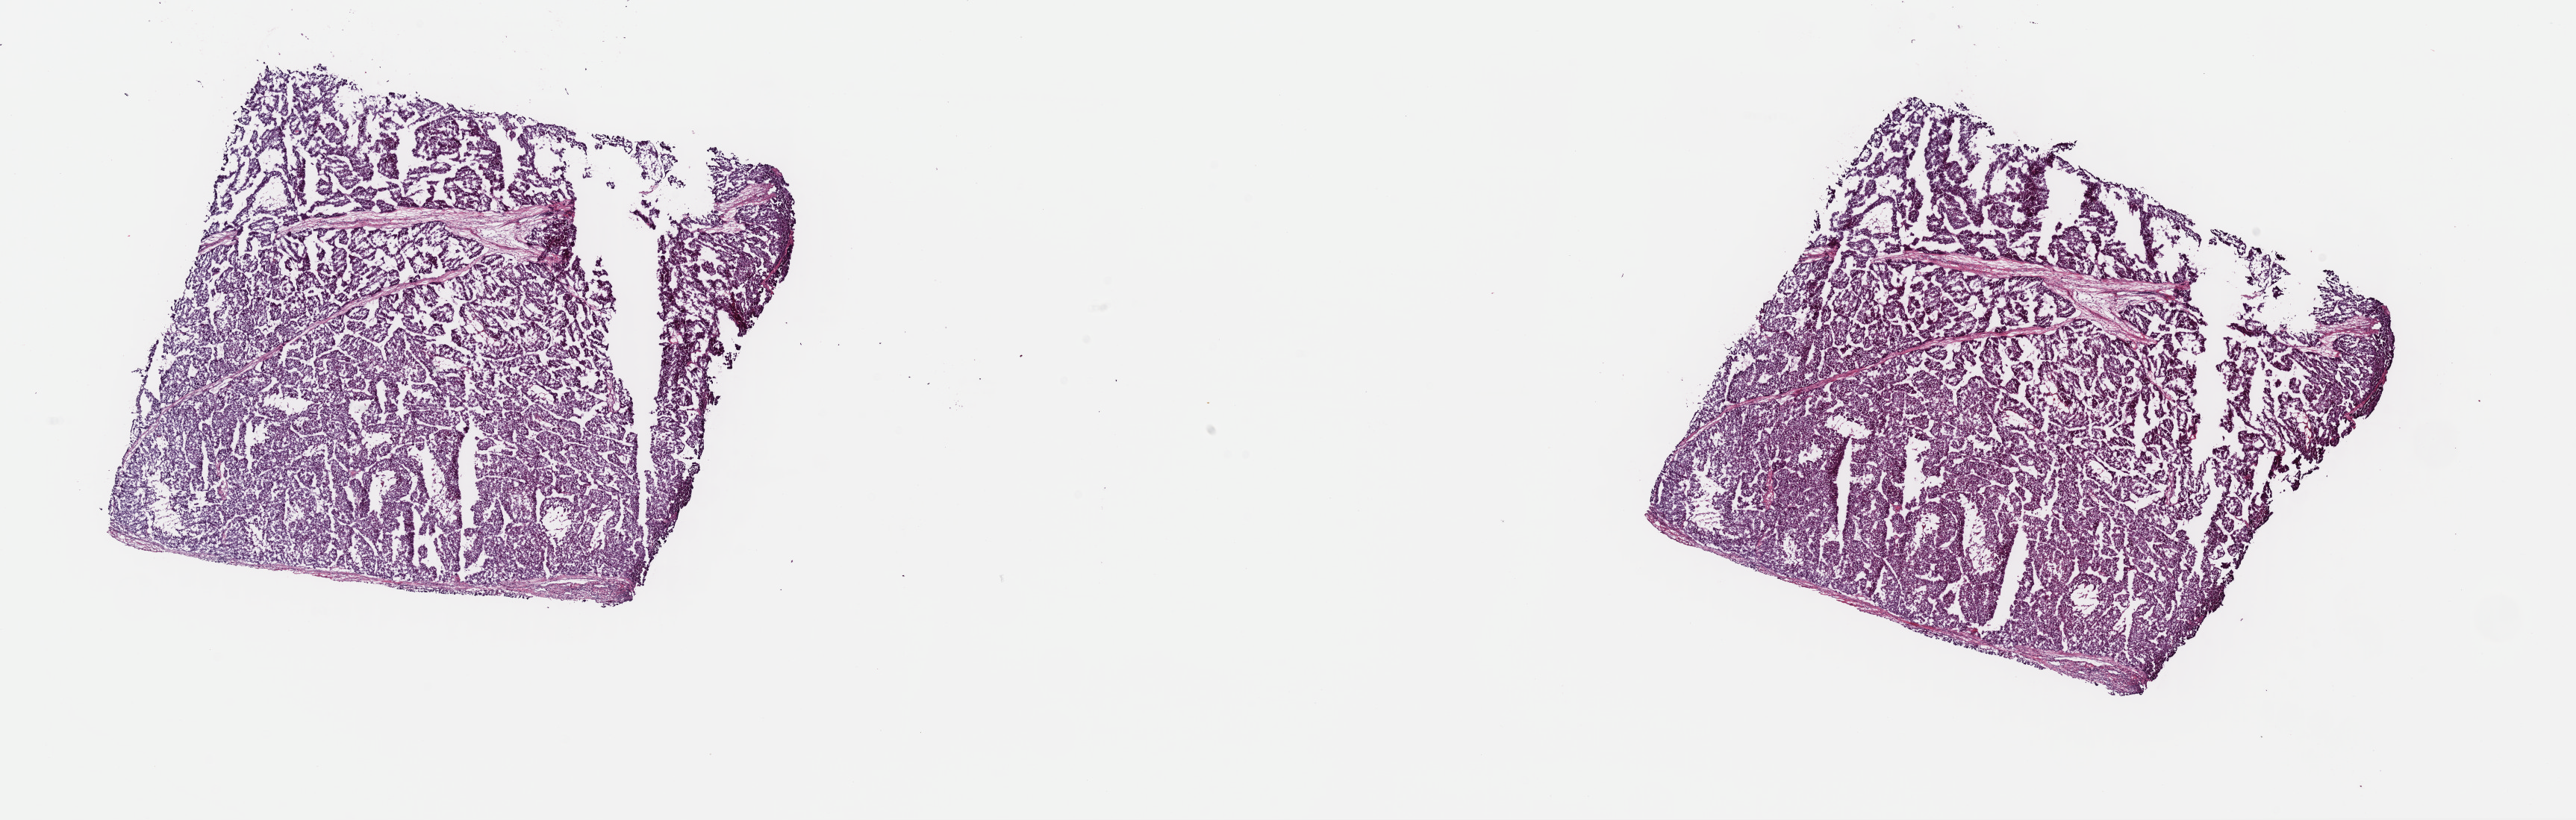
Whole-slide histology image, Hematoxylin and eosin (H&E) stained — shown as a low-resolution overview of the whole scanned area (about 27.3 x 8.7 mm, slide scanned at 40x), frozen section from the top of the tissue portion, primary tumour sample from the liver. Male, age 67 years at initial diagnosis. Histologic grade: G3 (poorly differentiated). Composition of this section per pathologist review: tumour cells 90%, tumour nuclei 90%, normal cells 0%, stromal cells 10%, necrosis 0%. Inflammatory infiltration, as recorded: lymphocyte infiltration 1%, monocyte infiltration 1%, neutrophil infiltration 0%.
• histologic diagnosis: Hepatocellular carcinoma, NOS
• AJCC pathologic stage: I (5th edition)